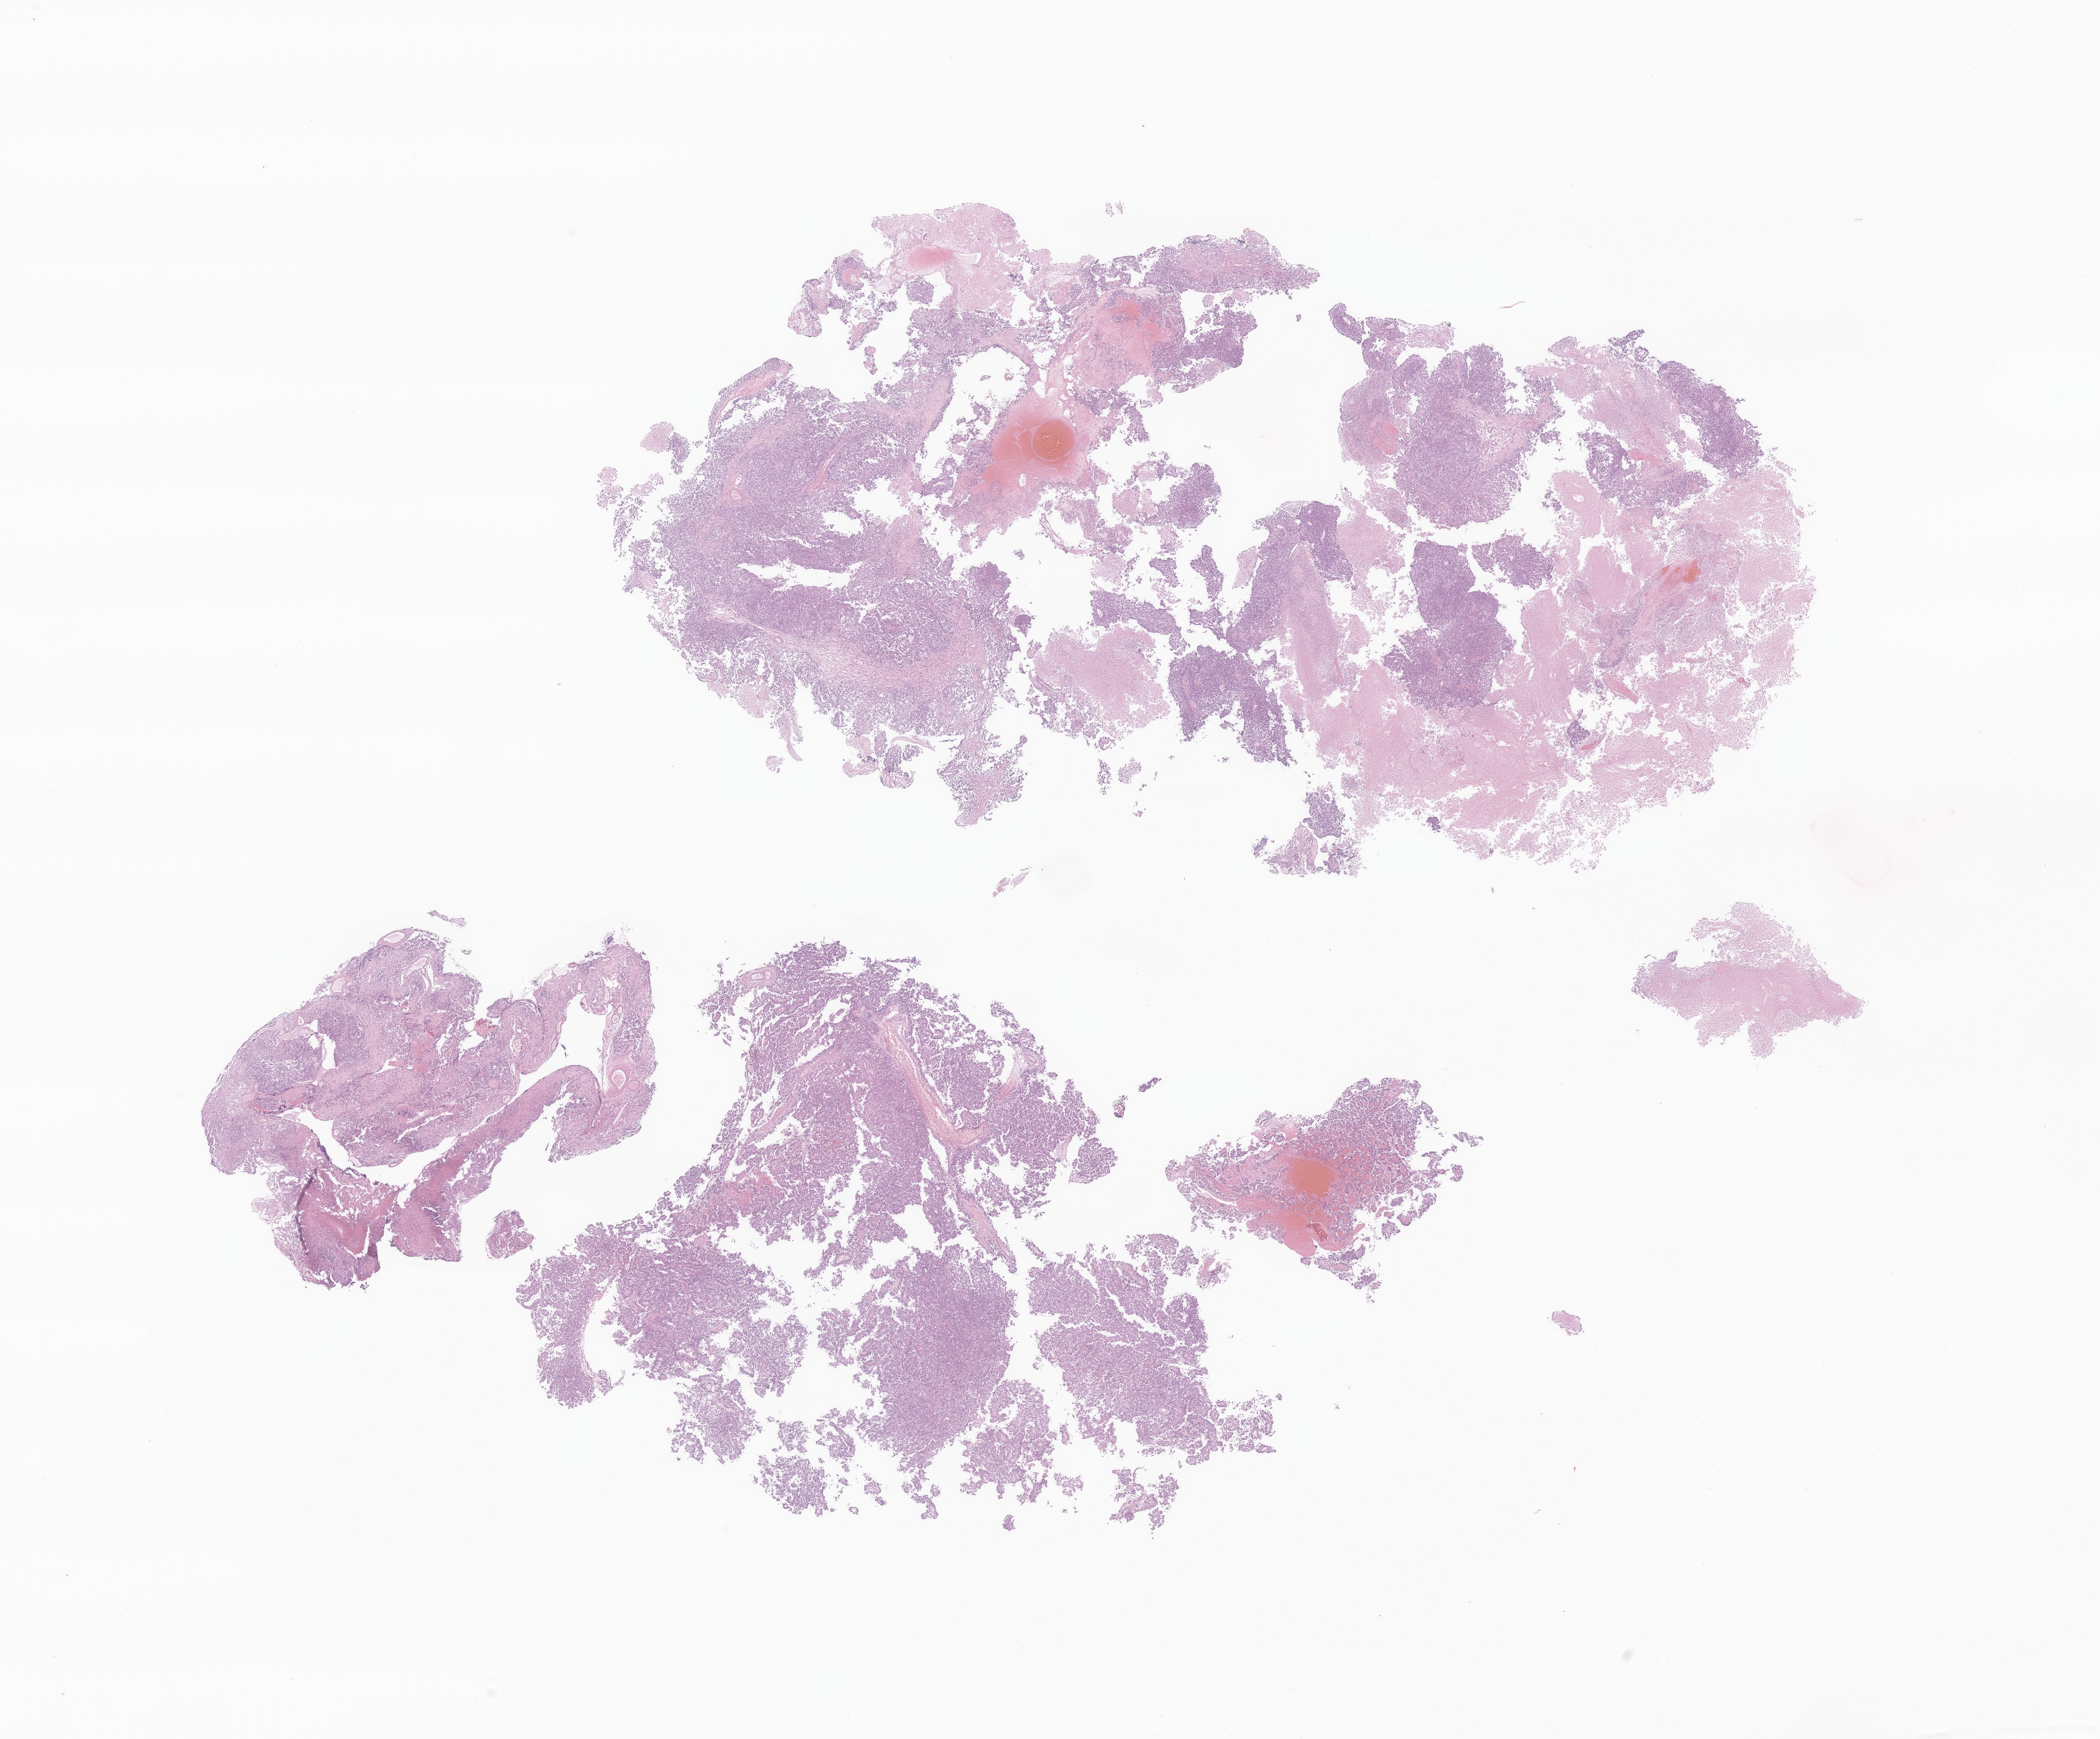
Haematoxylin and eosin whole-slide image of tumor tissue from the brain, a low-resolution overview of the entire scanned area, about 19.0 x 15.8 mm, FFPE section. Male patient, age 124 days.
• diagnosis: Glioma, malignant